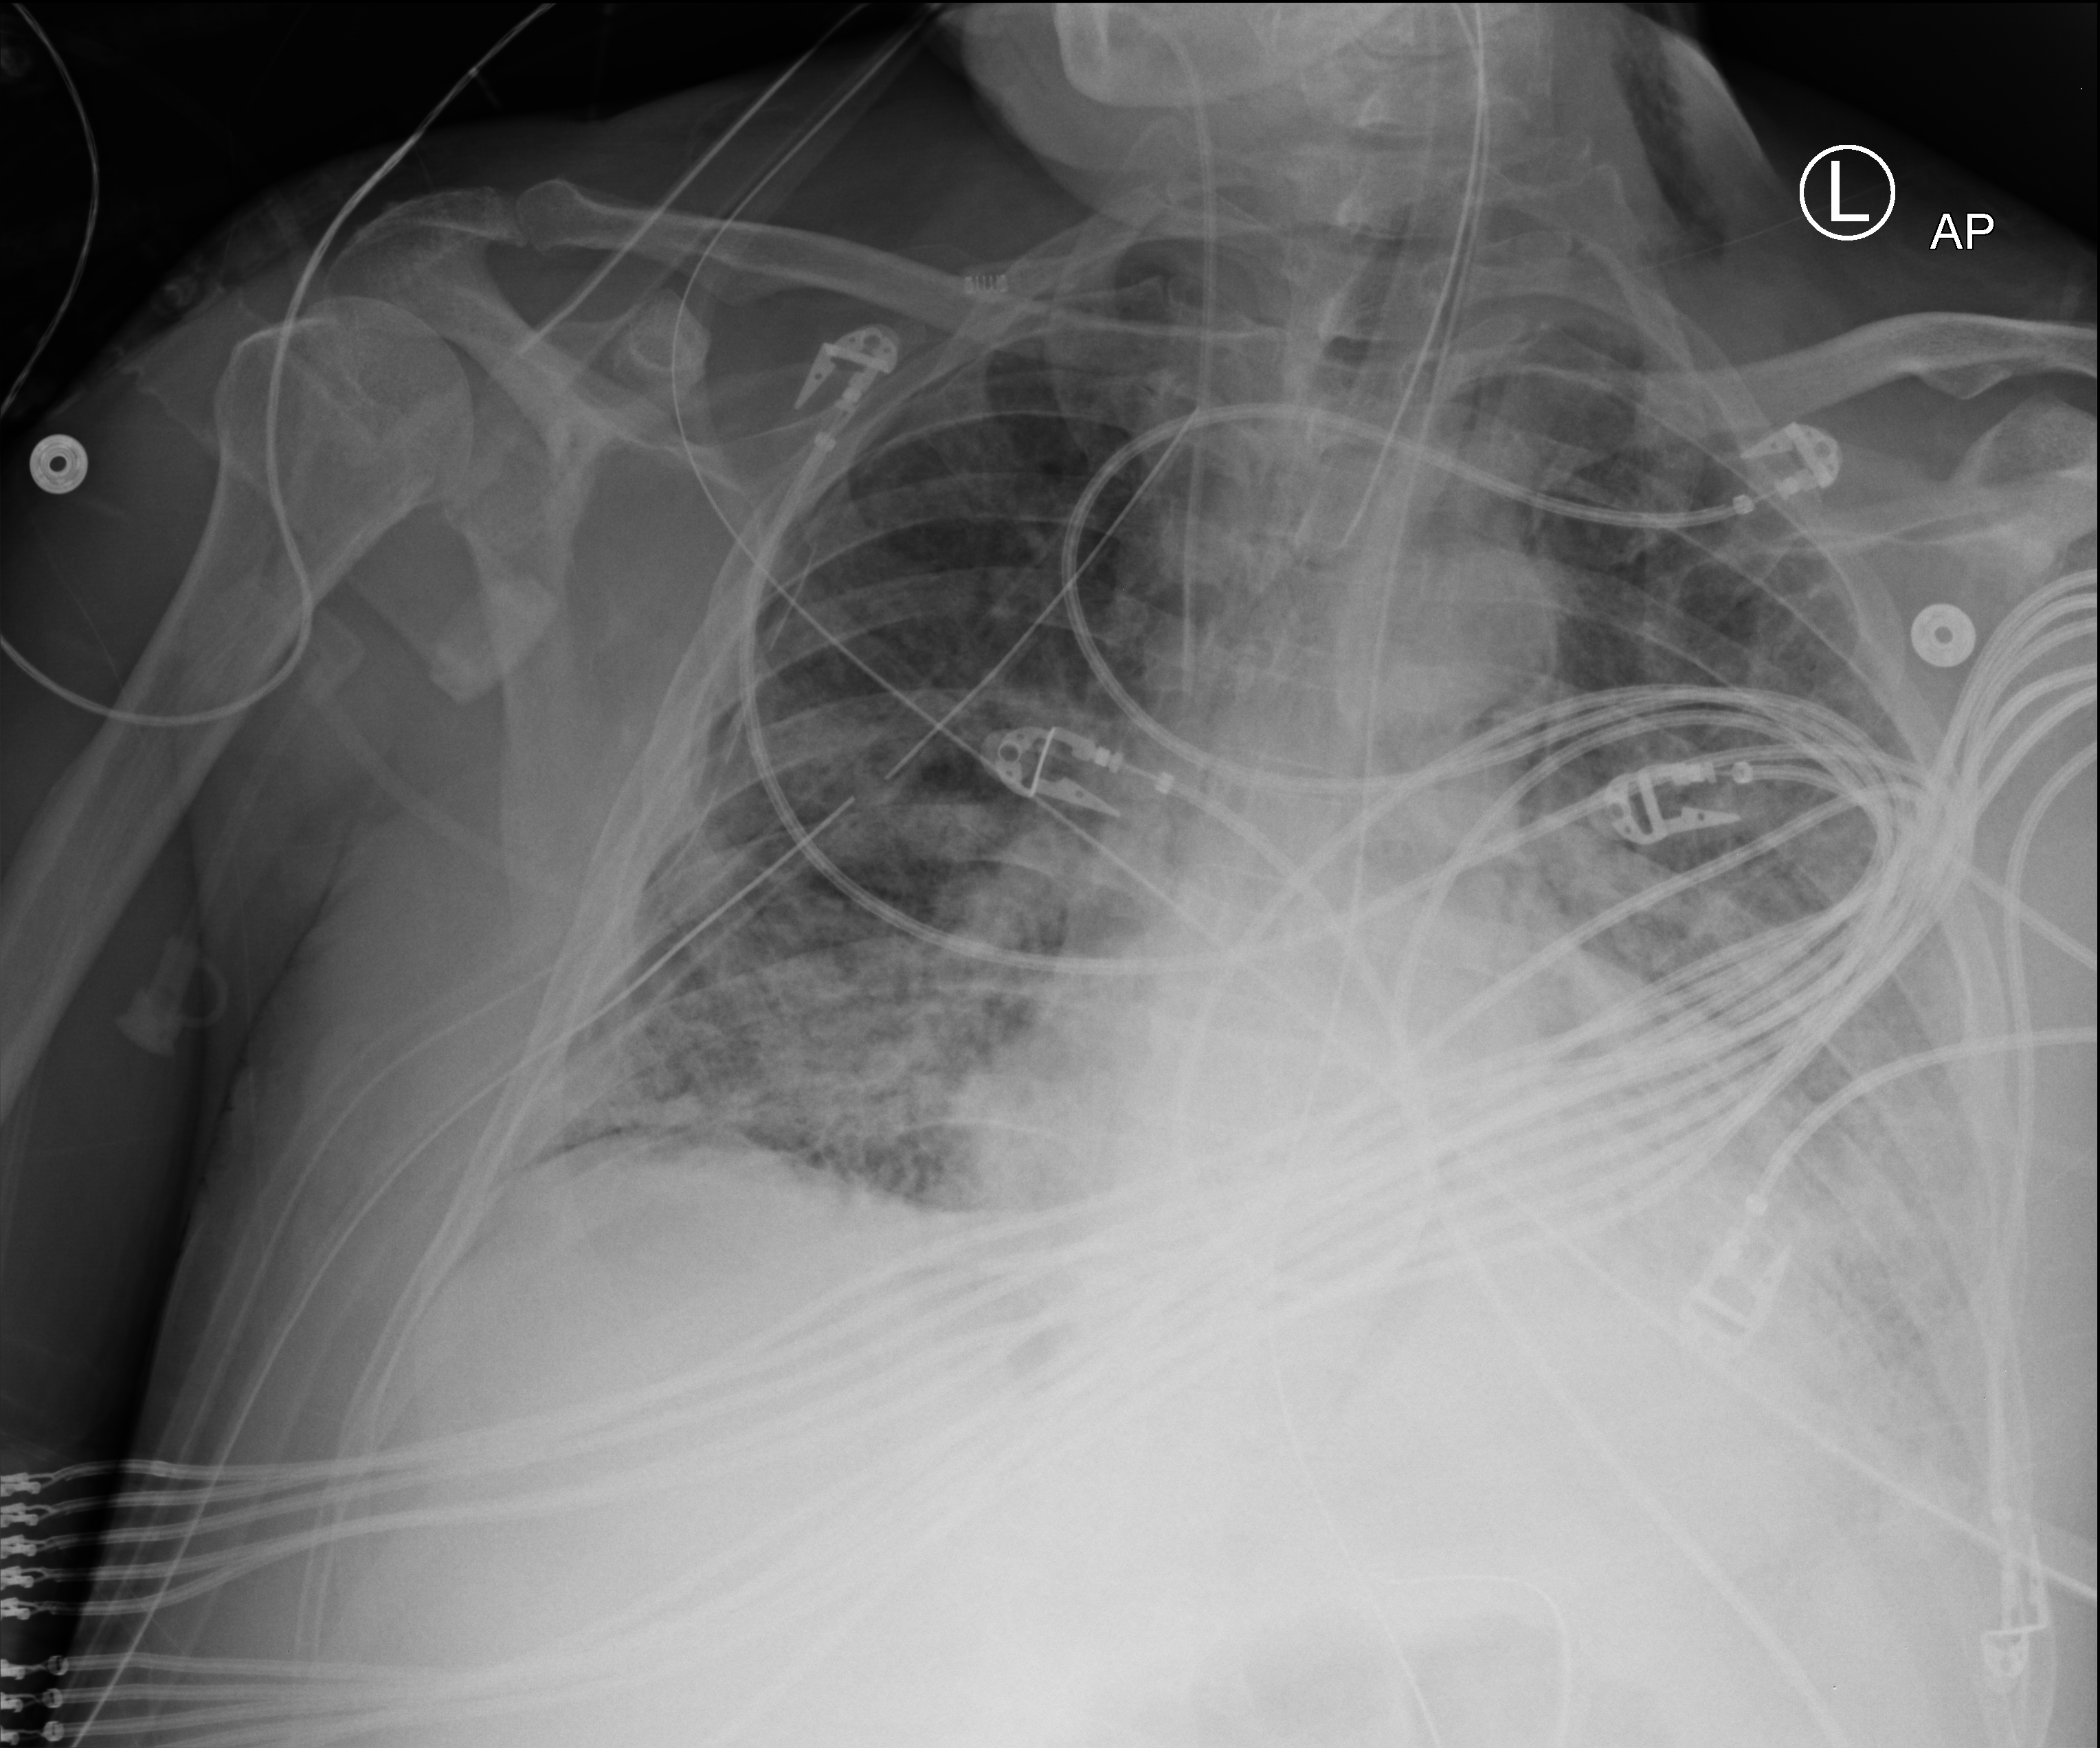
Chest X-ray (portable), anteroposterior (AP) projection. Patient hospitalised with COVID-19; male, aged 60–74 years.
Admission-level facts for this patient (not findings on this image; timing relative to this image not recorded): admitted to intensive care during this hospital stay: yes; hypertension (admission record): yes; mechanically ventilated during this hospital stay: yes.